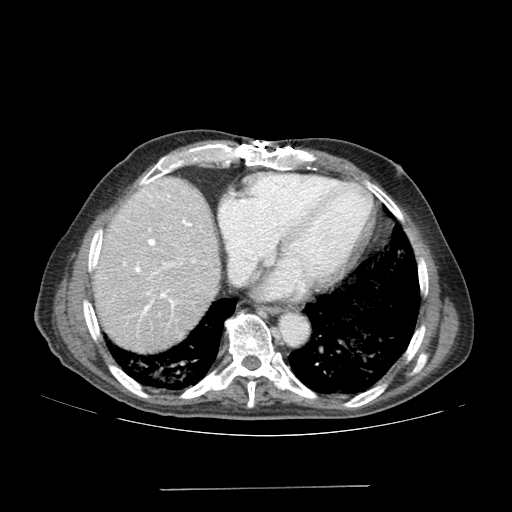
Contrast-enhanced abdominal CT (liver protocol), one axial slice. Position 152 of 192 along the scan axis. Reconstruction kernel SOFT. 120 kVp. Soft-tissue window (W 400 / L 40 HU). 2.5 mm slice thickness. 512 × 512 image matrix. From the clinical record (not read from this slice): diagnosis: hepatocellular carcinoma (patient treated with transarterial chemoembolisation; whether this scan precedes or follows treatment is not stated here); TNM stage (as recorded): Stage-IVA; Child-Pugh class: A; tumour differentiation: poorly differentiated; tumour nodularity: uninodular.
Structures marked on this image (semi-automatically segmented with operator editing):
- liver parenchyma outside the tumour (the mass and vessels are separate outlines, so this box may not span the whole liver): bounding box <94,178,220,352> (left, top, right, bottom; pixels)
- liver vessels: <124,219,194,314>